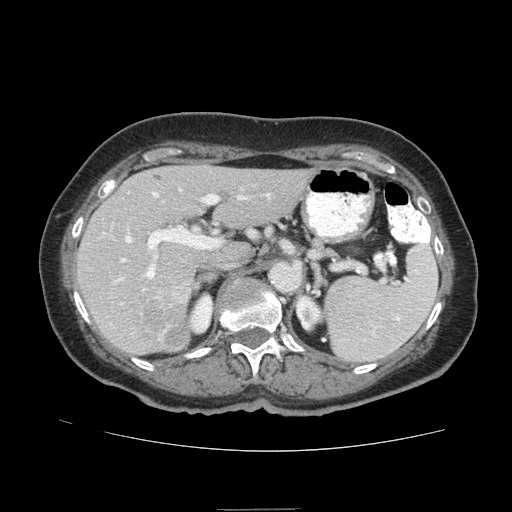
Contrast-enhanced abdominal CT (liver protocol), one axial slice. Position 47 of 95 along the scan axis. Reconstruction kernel STANDARD. 140 kVp. Soft-tissue window (W 400 / L 40 HU). 2.5 mm slice thickness. 512 × 512 image matrix, field of view 360 × 360 mm. From the clinical record (not read from this slice): diagnosis: hepatocellular carcinoma (patient treated with transarterial chemoembolisation; whether this scan precedes or follows treatment is not stated here); TNM stage (as recorded): Stage-IVA.
Outlined on this slice (semi-automatically segmented with operator editing):
- liver parenchyma outside the tumour (the mass and vessels are separate outlines, so this box may not span the whole liver): bounding box <76,164,315,354> (left, top, right, bottom; pixels)
- mass: <138,293,190,350>
- liver vessels: <116,188,270,304>